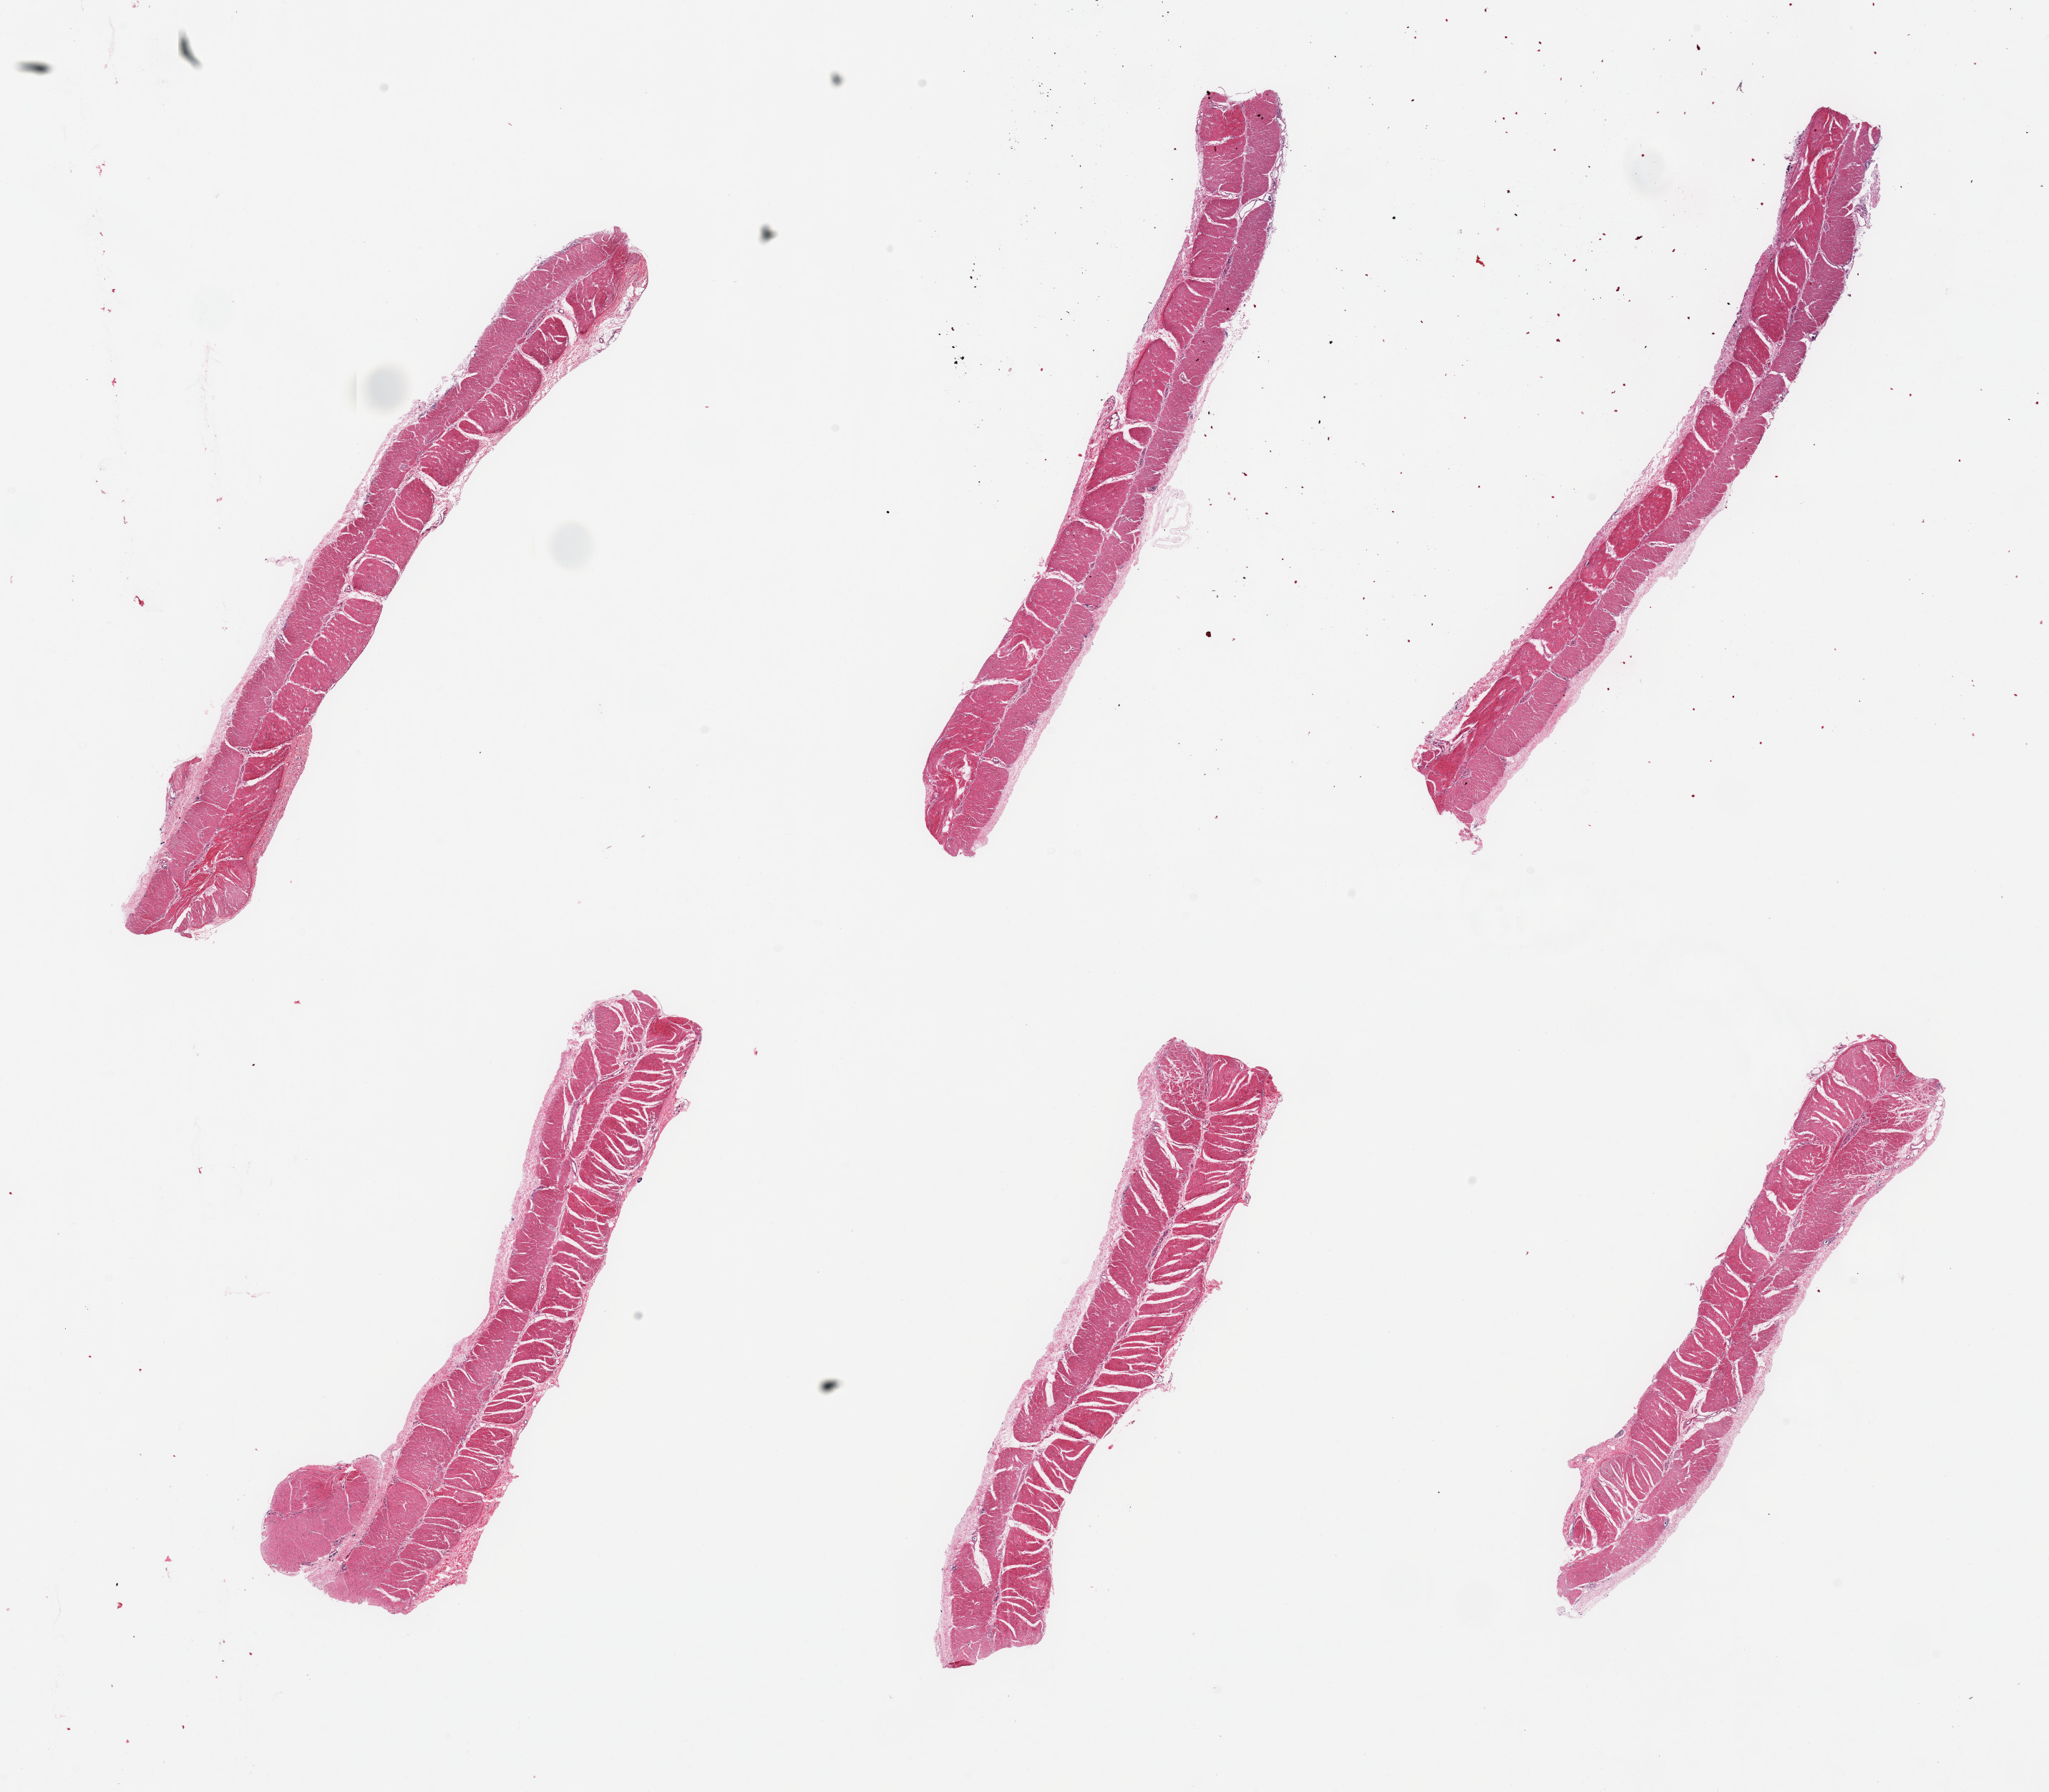
Digitized H&E-stained section — whole scanned area (about 22.6 x 19.8 mm, acquisition: 20x scan) shown as a low-resolution overview, PAXgene-fixed paraffin-embedded (PFPE) section, section of ileum (target tissue), tissue donor sample. Donor sex: male.
Reviewer comment on this tissue sample: 6 pieces; muscle only, no mucosa.